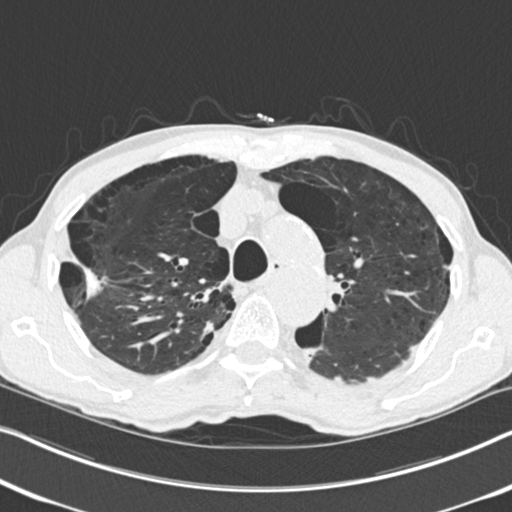
Low-dose screening chest CT, one axial slice; position 183 of 251 along the scan axis; reconstruction kernel B30f; lung window (W 1500 / L -600 HU); 2 mm slice thickness; 512 × 512 image matrix.
Structures marked on this image (outlined manually by an expert reader):
- lesion 1 (tumor, upper lobe of right lung): box from (x=84, y=269) to (x=102, y=298) px